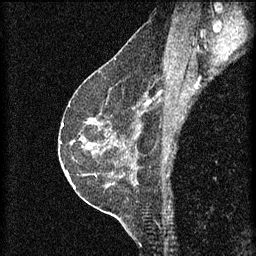
Breast MRI (dynamic contrast-enhanced), one sagittal slice. Position 36 of 60 along the scan axis. 3 images stored at this slice position (order not interpretable as contrast timing). 1.5 T. TE 4.2 ms, TR 8.2 ms. 2 mm slice thickness. 256 × 256 image matrix, field of view 180 × 180 mm. Patient: female, 60 years.
Outlined on this slice (semi-automatically segmented with operator editing):
- analysis volume of interest (the breast-tissue region the enhancement analysis was run in; not a lesion): box from (x=74, y=124) to (x=113, y=155) px
- tumour enhancement mask (voxels above the 70 % enhancement threshold inside the analysis volume of interest): (x=88, y=124)–(x=93, y=125)